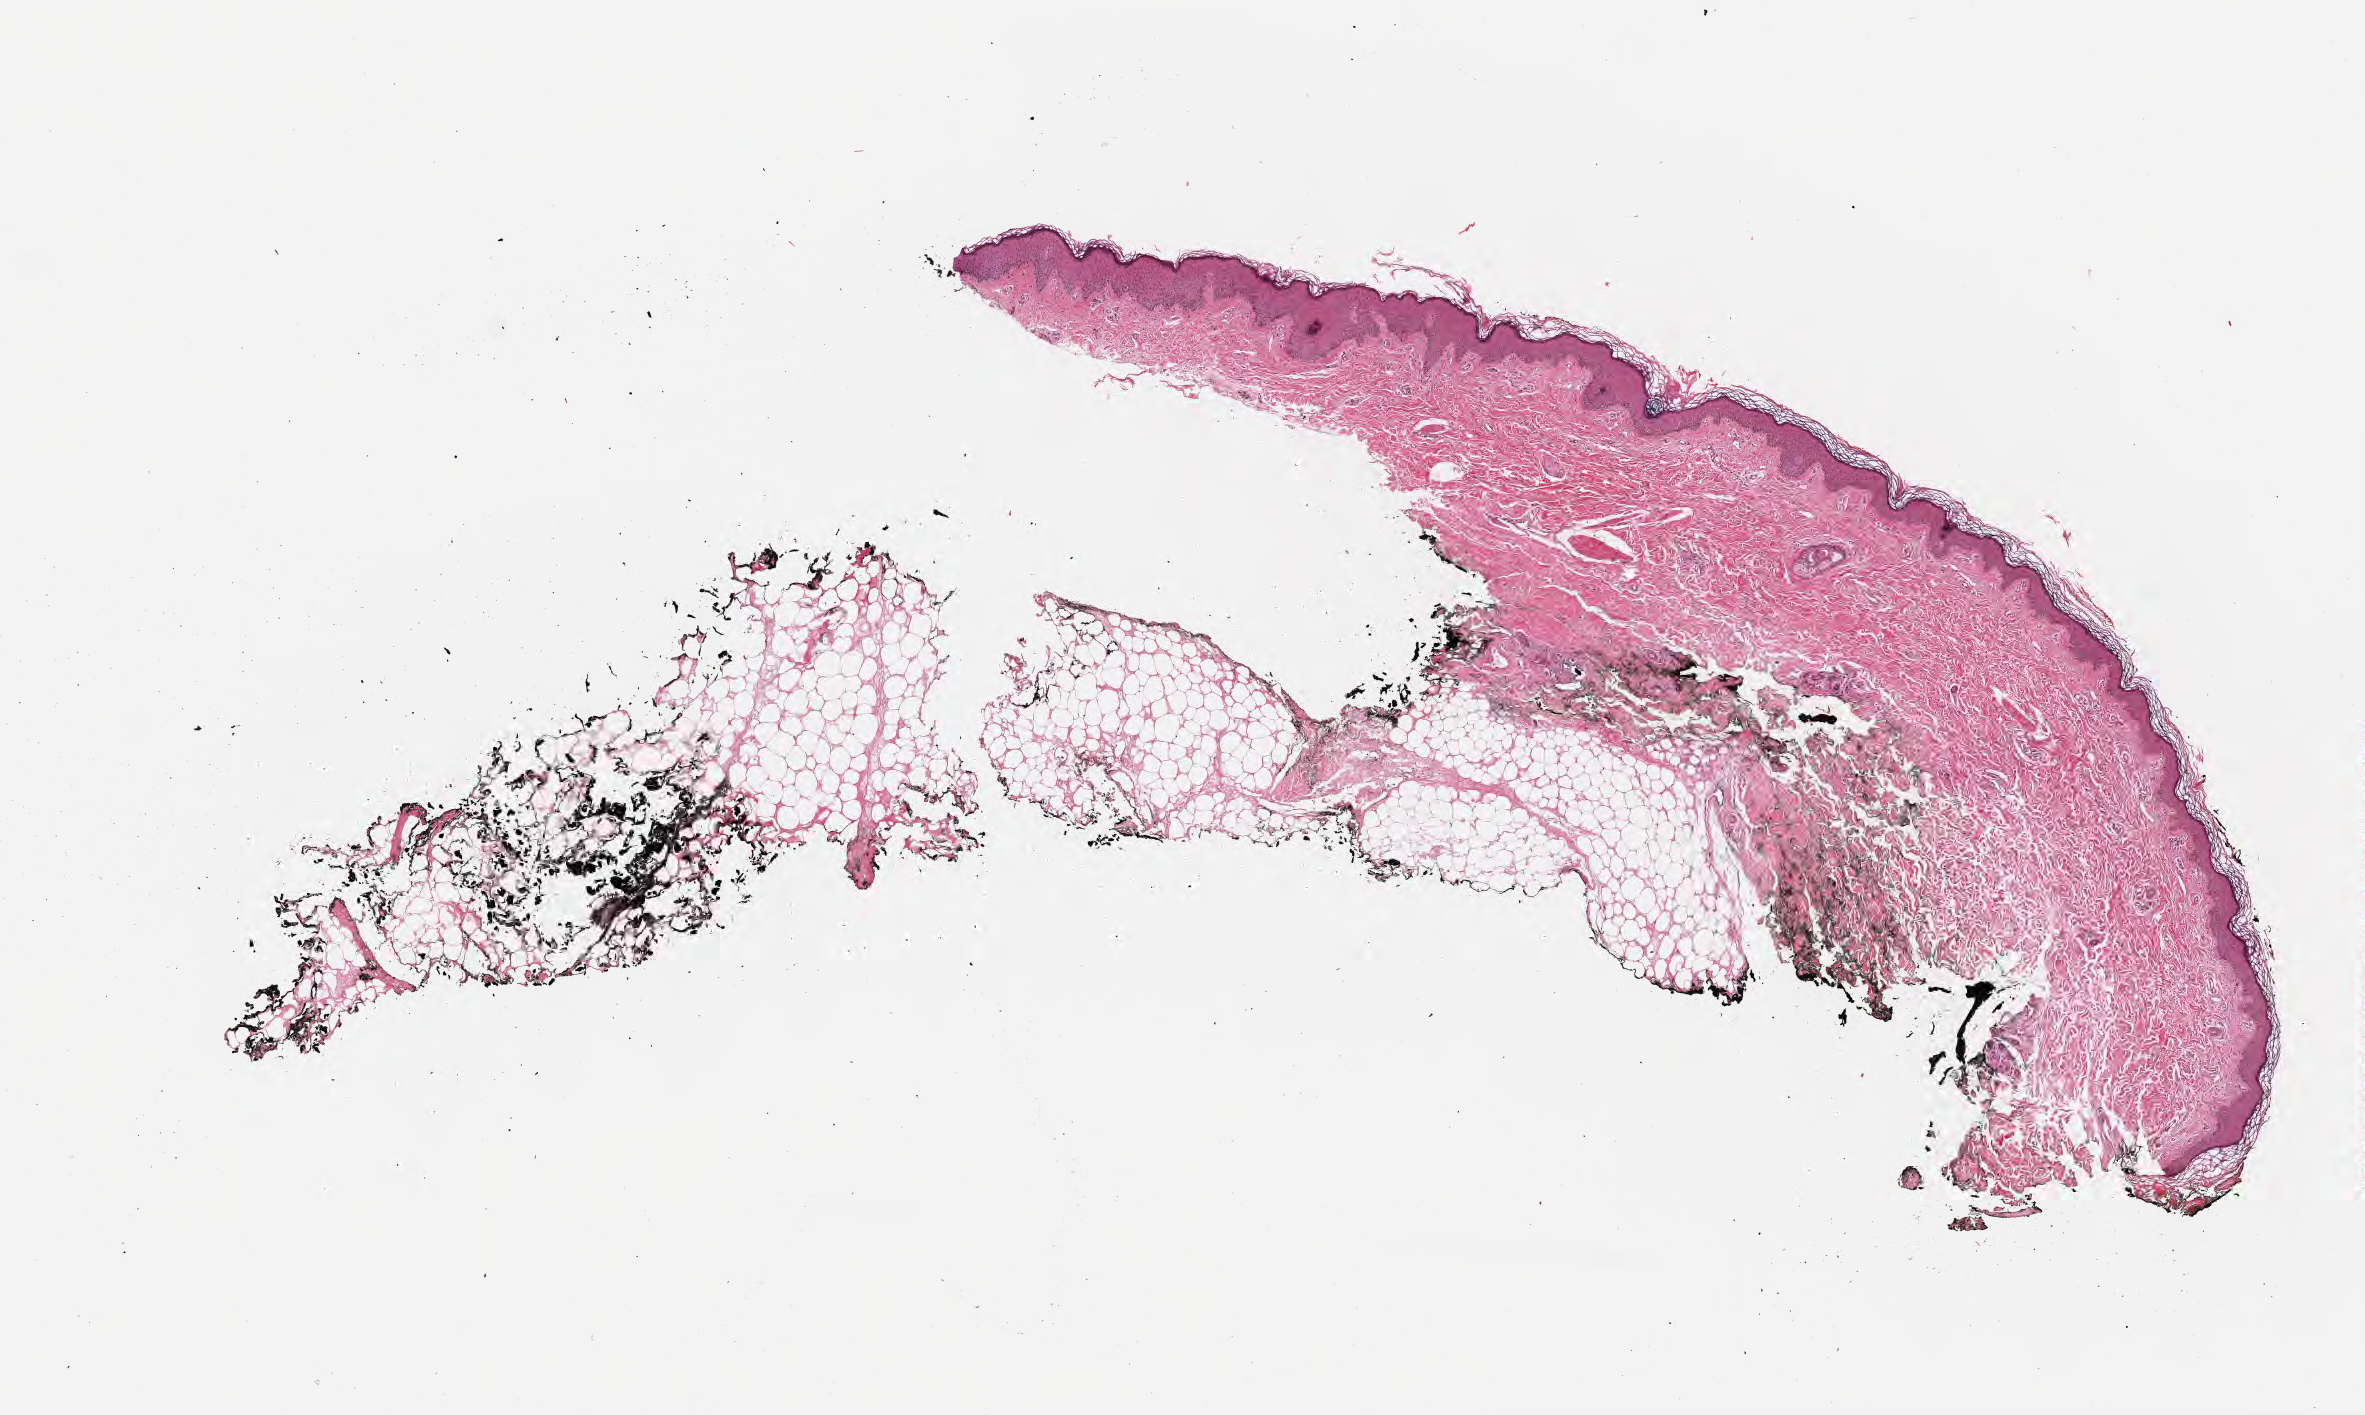
H&E whole-slide image — a low-resolution overview of the entire scanned area, about 9.6 x 5.7 mm. Formalin-fixed, paraffin-embedded (FFPE) tissue. Specimen: non-tumor (normal tissue) sample from a patient with burkitt lymphoma, NOS. Patient female; age 16 years. Composition of this section per pathologist review: tumor cells 0%, tumor nuclei 0%.
This section: non-tumor tissue sample; the patient's diagnosis is given above. Section: bottom of the tissue portion.